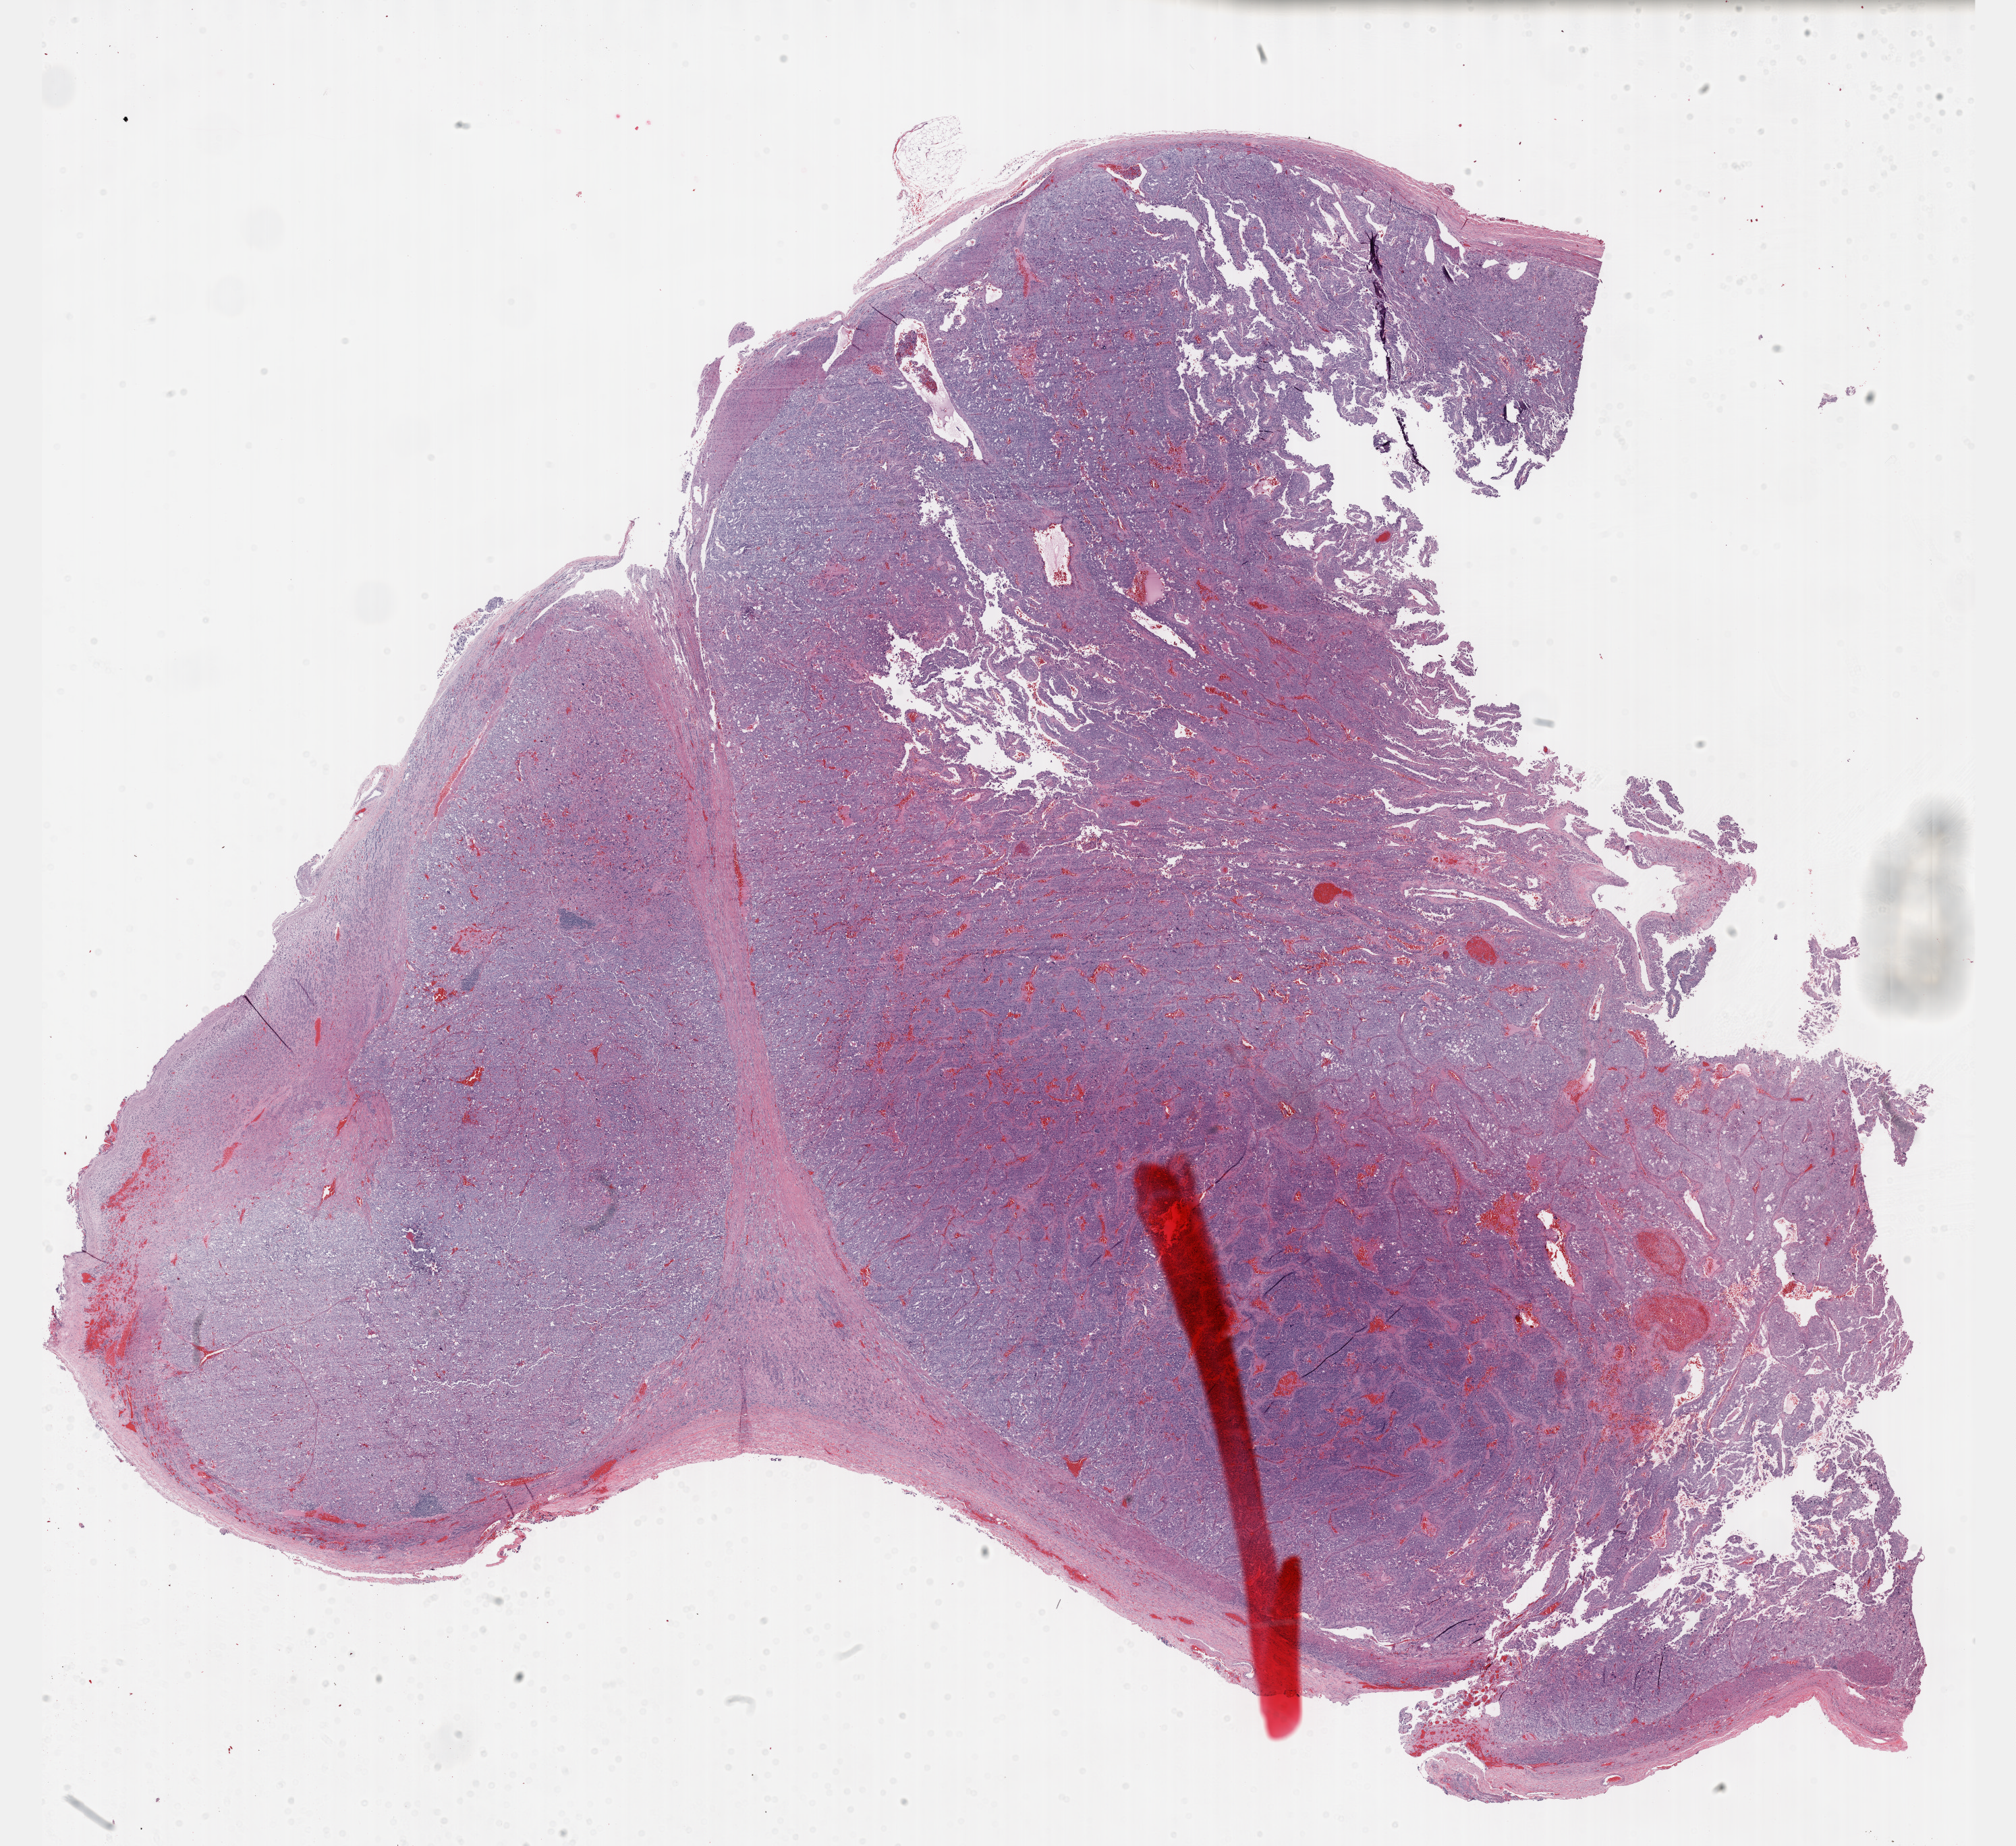
Digitized Hematoxylin and eosin (H&E) stained tissue section (whole slide), a low-resolution overview of the entire scanned area, about 24.1 x 22.1 mm (acquisition: 40x scan), FFPE section, sample: primary tumour, adrenal gland. Female, age 35 years at initial diagnosis.
Histologic diagnosis: Pheochromocytoma, NOS.